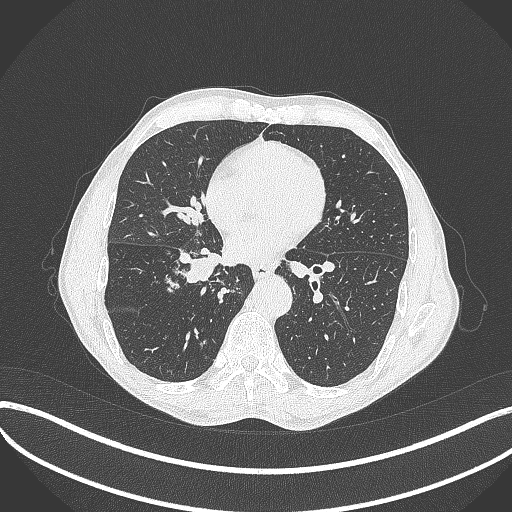
Chest CT, one axial slice; position 190 of 481 along the scan axis; reconstruction kernel B70f; 120 kVp; lung window (W 1500 / L -600 HU); 1 mm slice thickness; 512 × 512 image matrix. Patient: male, 65 years. Case-level facts recorded for this patient, not image findings: clinical TNM (as recorded): T2a N0 M0.
Structures marked on this image (rectangle marked by the reading radiologist):
- lung tumour (recorded histology: squamous cell carcinoma): bounding box [x1, y1, x2, y2] px = [169, 243, 227, 287]